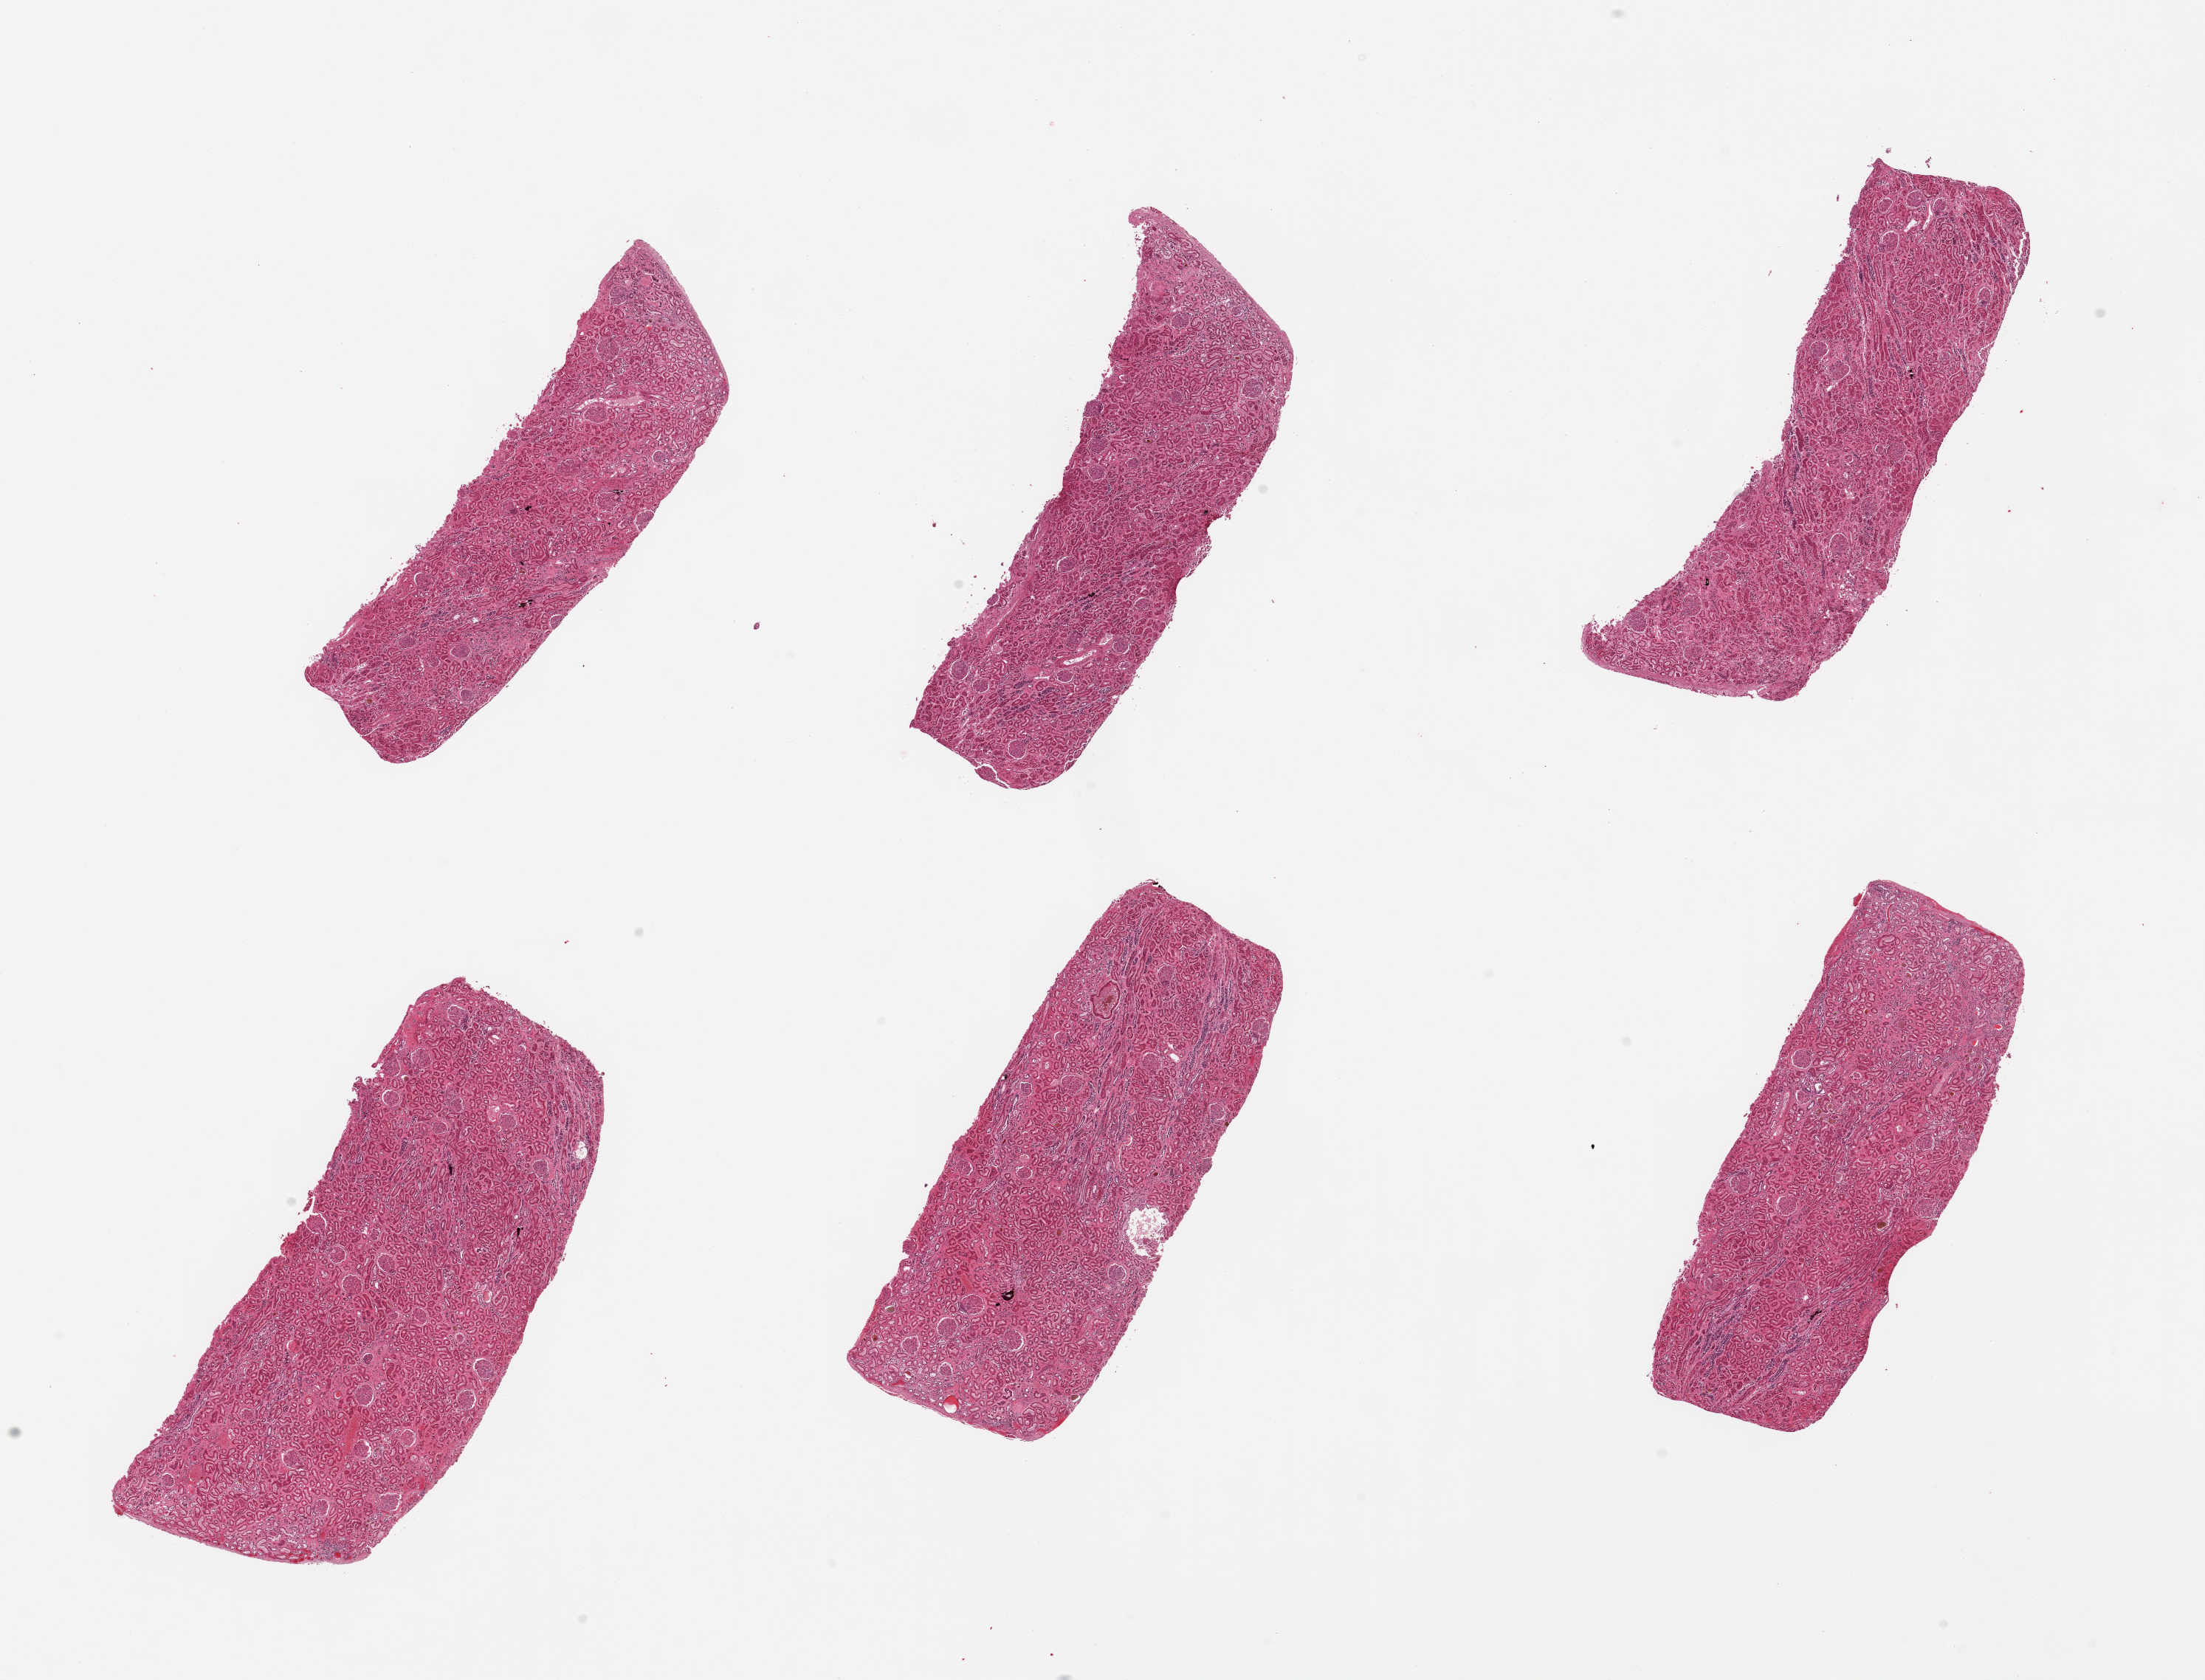
Haematoxylin and eosin whole-slide image, a low-resolution overview of the entire scanned area, about 23.6 x 18.0 mm; PAXgene-fixed paraffin-embedded (PFPE) section; section of renal cortex (target tissue); tissue donor sample. Donor sex: male.
- pathologist's review note for this sample: 6 pieces, glomeruli present, tubules autolyzed